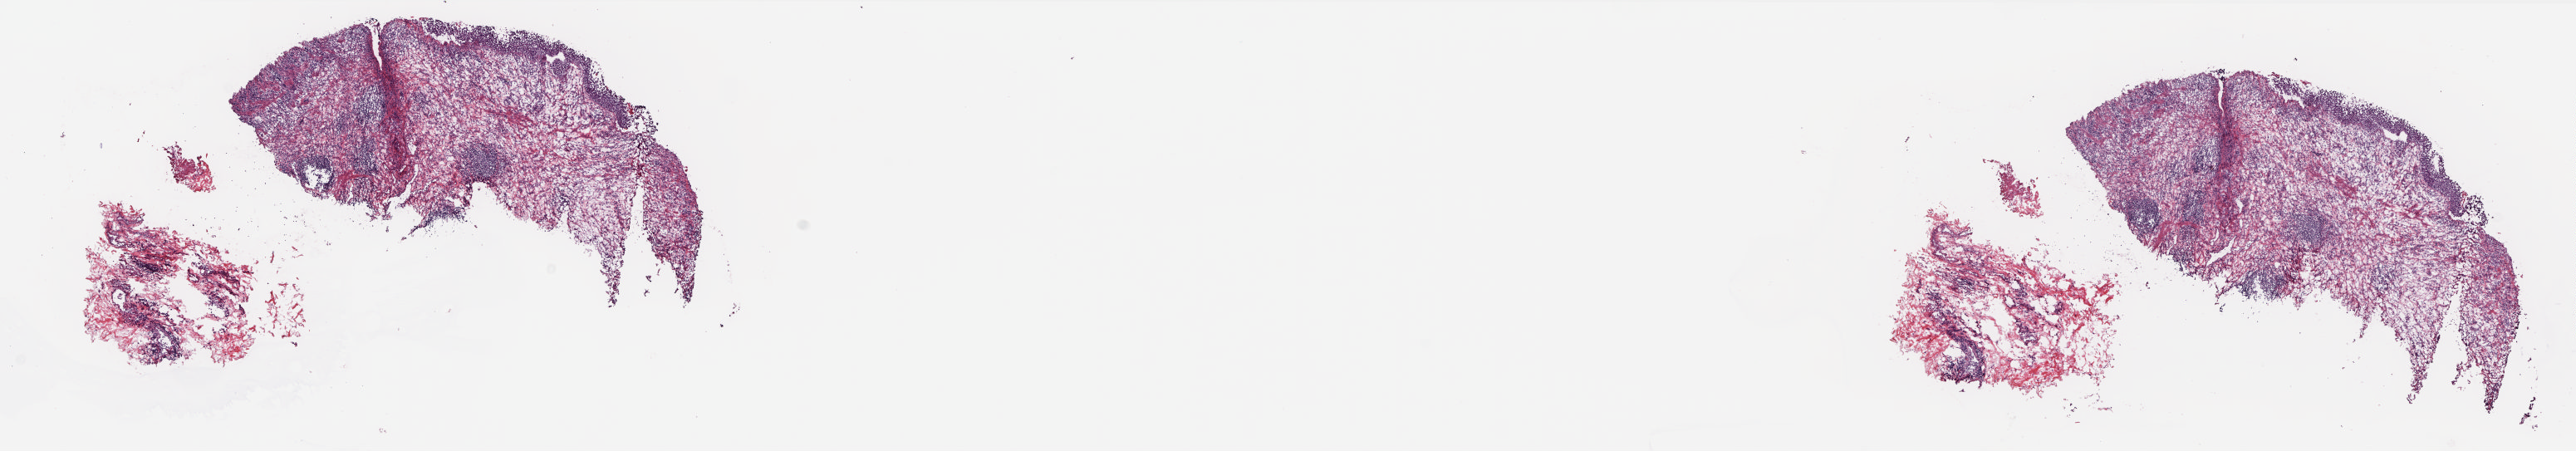
Whole-slide histology image, H&E — shown as a low-resolution overview of the whole scanned area (about 25.0 x 4.4 mm, slide scanned at 20x); frozen section; solid tissue normal (non-tumour tissue) sample from the bladder. Patient sex: female. Pathologist review of this section (percent, as recorded): tumour cells 0%, tumour nuclei 0%, normal cells 12%, stromal cells 88%, necrosis 0%. Infiltration values recorded for this section: lymphocyte infiltration 65%, monocyte infiltration 1%, neutrophil infiltration 1%.
- this section: solid tissue normal (non-tumour) sample from the same patient
- patient diagnosis: Transitional cell carcinoma